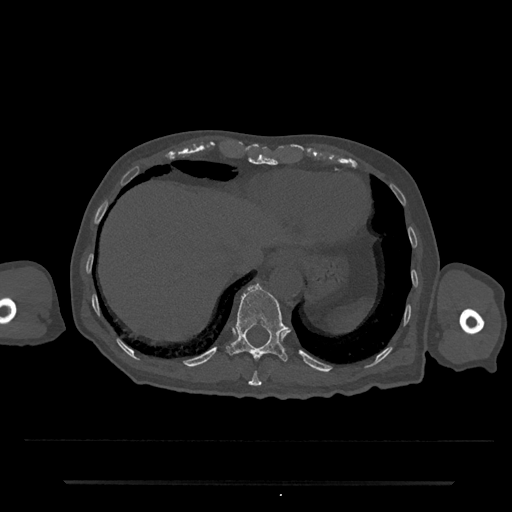
CT including the spine, one axial slice. Slice 261 of 797 in the series (ordered by position). Reconstruction kernel Br40s/3. 120 kVp. Bone window (W 1800 / L 400 HU). 512 × 512 image matrix, field of view 427 × 427 mm. Patient: male, 74 years. Case-level facts recorded for this patient, not image findings: primary cancer: prostate.
Annotated regions visible in this slice (semi-automatically segmented with operator editing):
- T10 vertebra: bounding box (x1, y1, x2, y2) in pixels: (248, 371, 262, 386)
- T11 vertebra: (225, 284, 289, 362)